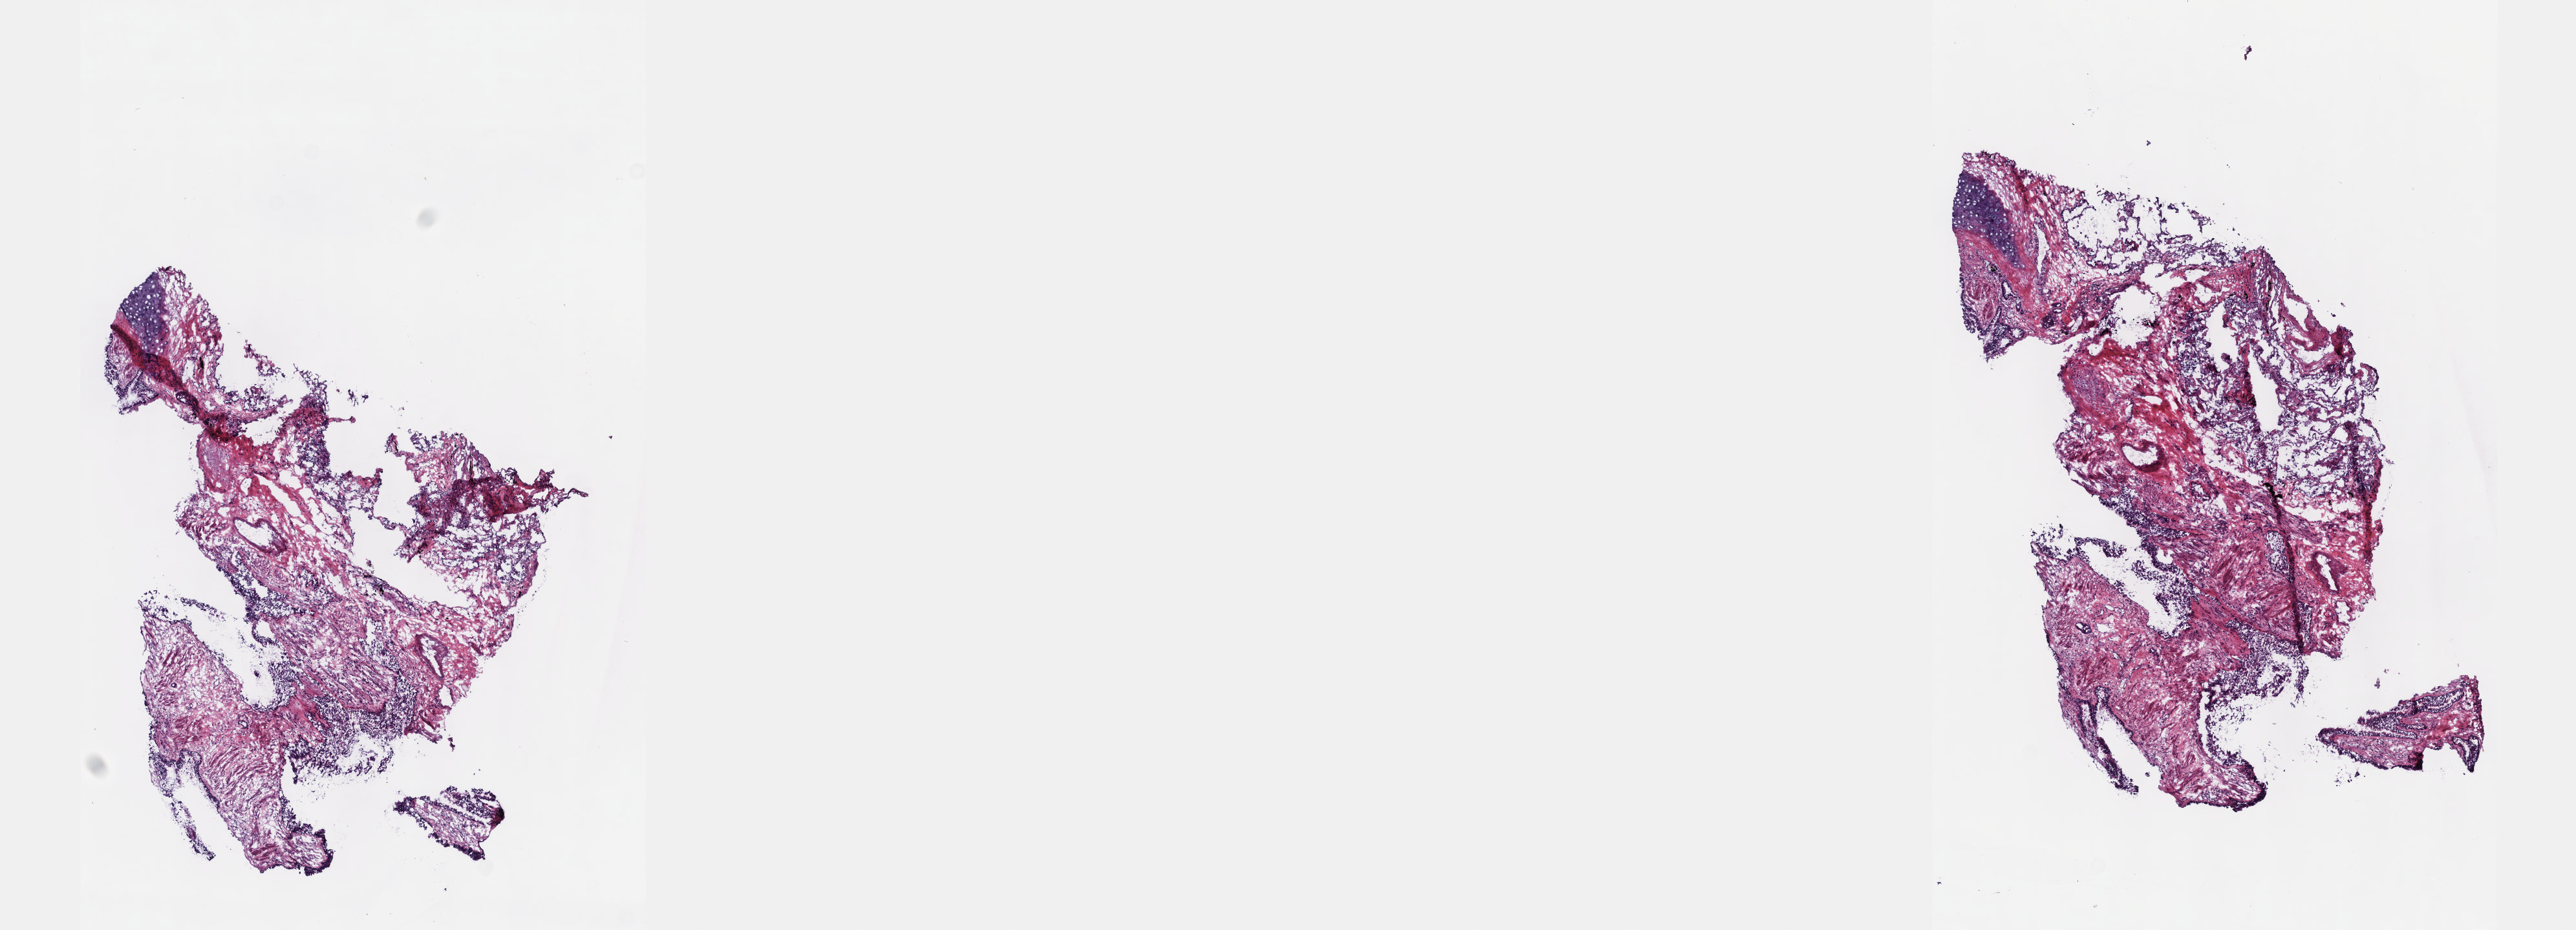
Whole-slide histology image, Hematoxylin and eosin (H&E) stained — a low-resolution overview of the entire scanned area, about 16.1 x 5.8 mm; frozen section from the top of the tissue portion; primary tumour sample from the lung. Male, age 68 years at initial diagnosis. Pathologist review of this section (percent, as recorded): tumour cells 70%, tumour nuclei 70%, normal cells 3%, stromal cells 27%, necrosis 0%. Inflammatory infiltration, as recorded: lymphocyte infiltration 3%, monocyte infiltration 1%, neutrophil infiltration 3%.
AJCC pathologic stage: IA (5th edition). Laterality: left. Histologic diagnosis: Adenocarcinoma, NOS.